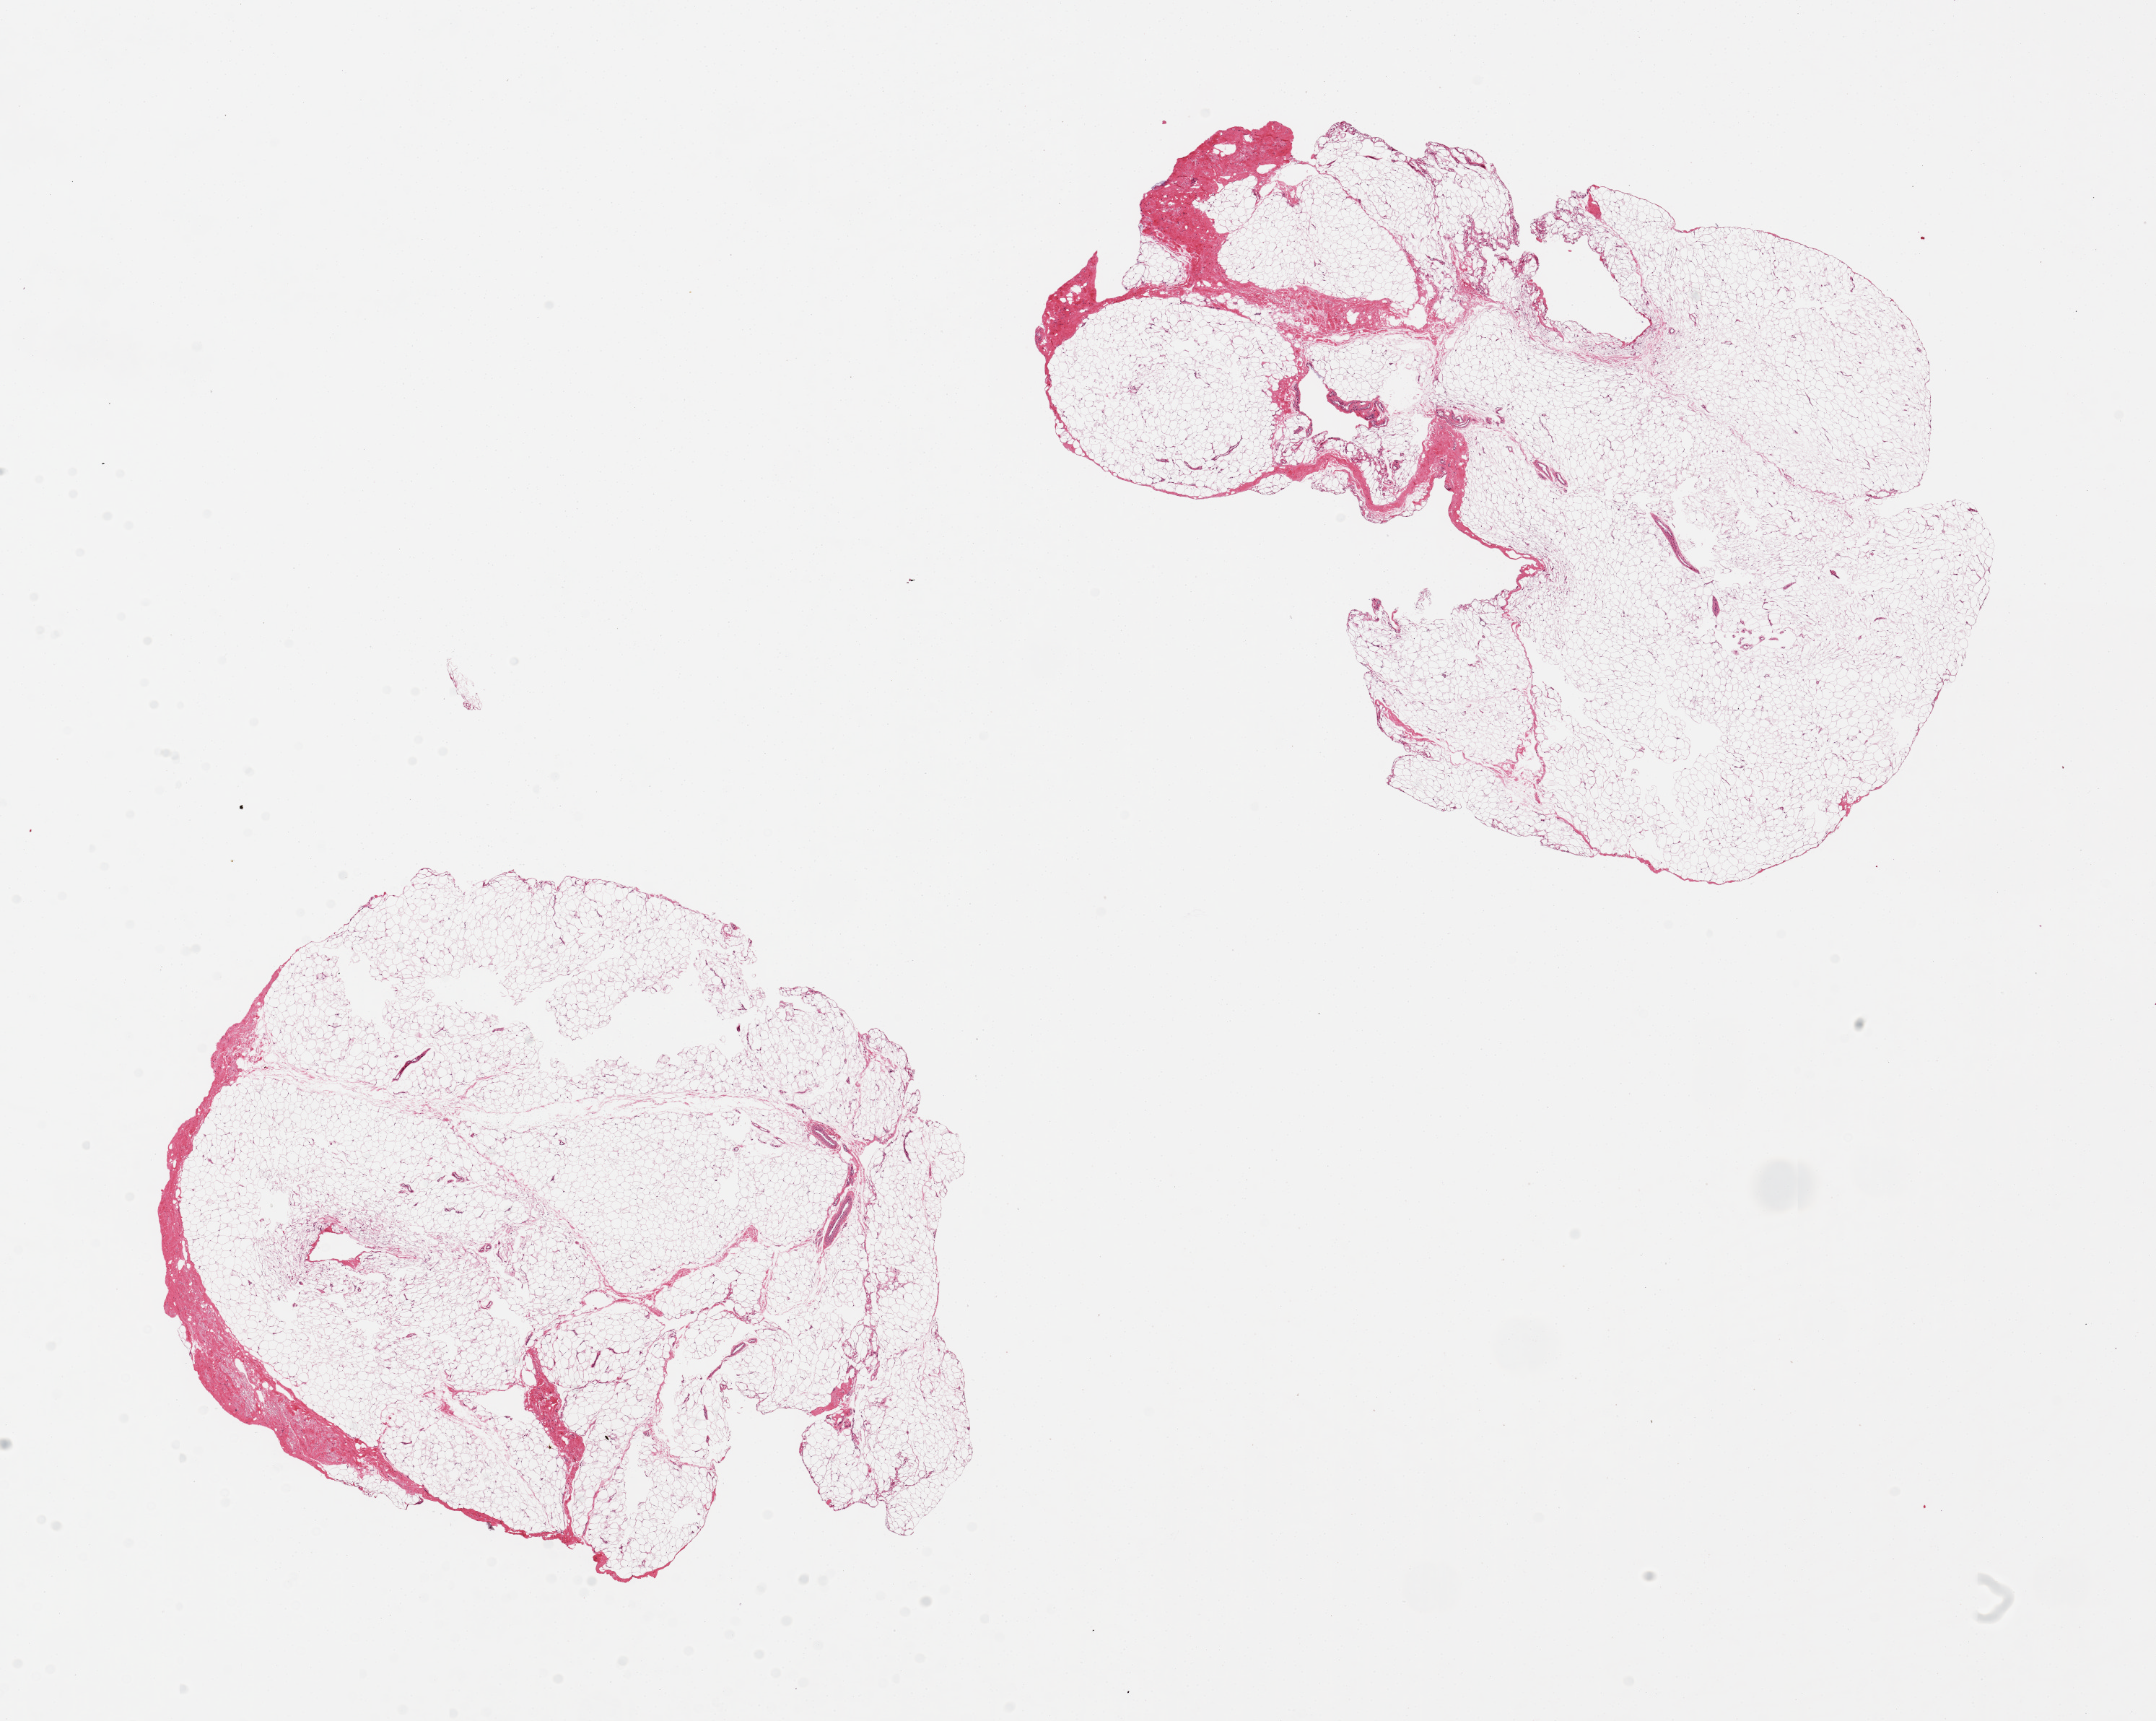
Digitized haematoxylin and eosin-stained section — shown as a low-resolution overview of the whole scanned area (about 23.6 x 18.9 mm), PAXgene-fixed, paraffin-embedded tissue, sampled site (target tissue): adipose tissue, donor tissue sample. Female donor.
Reviewer comment on this tissue sample: 2 pieces, 11x7.5 & 9.5x8mm.